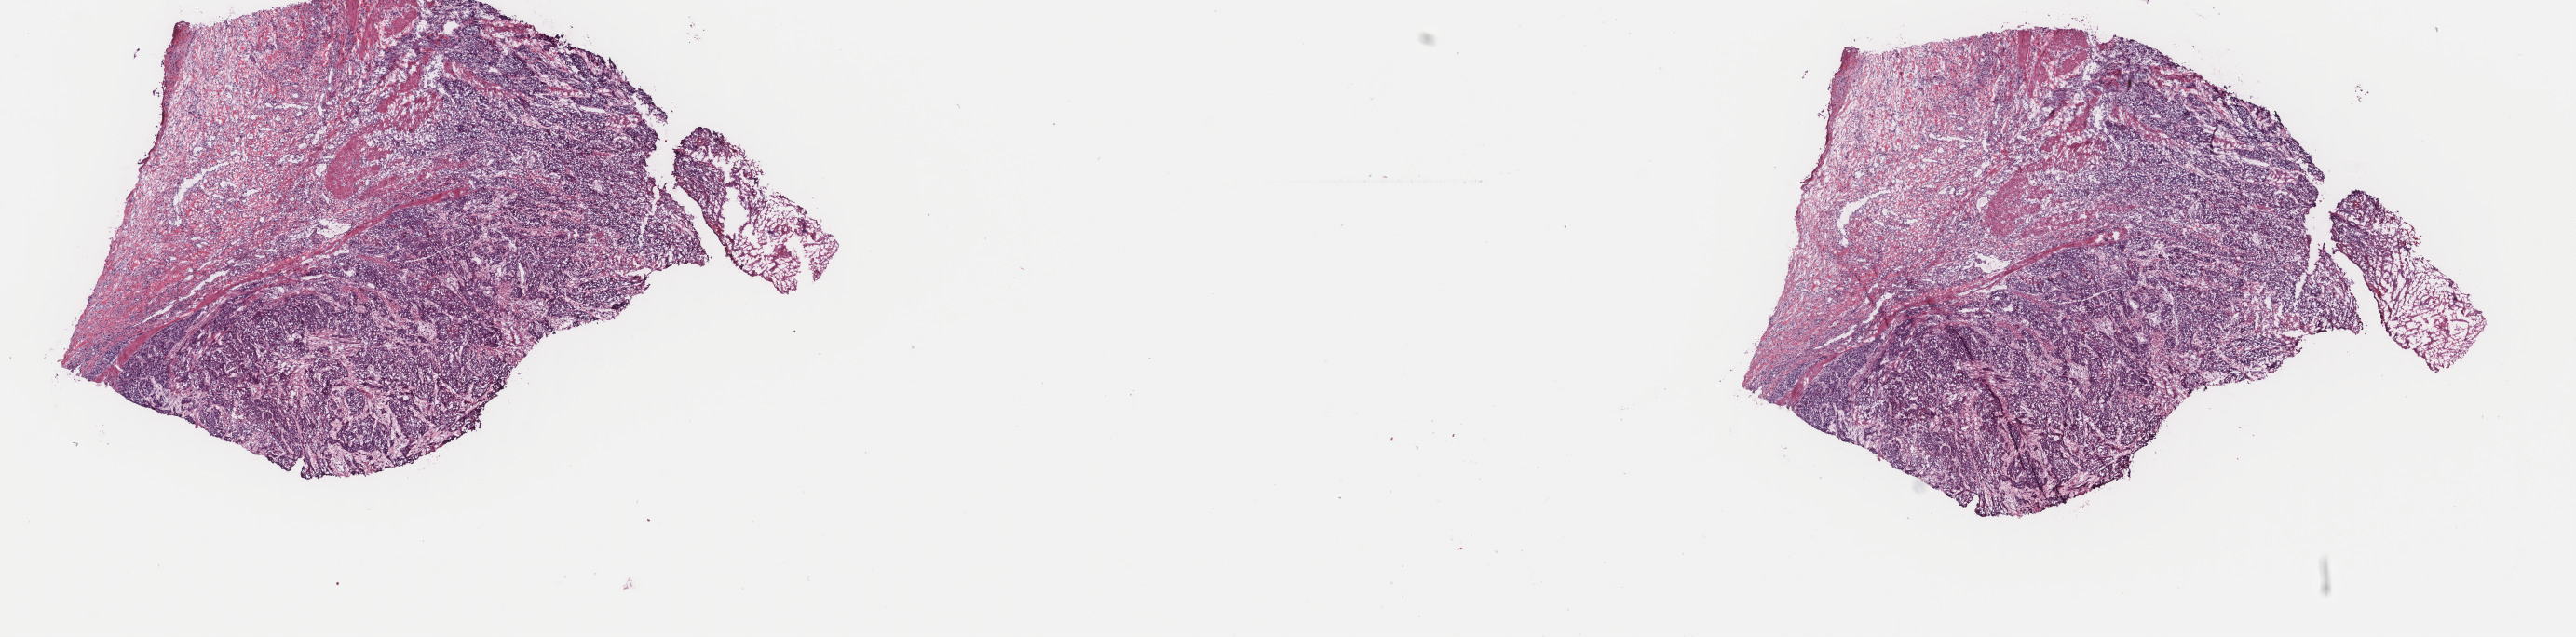
Whole-slide histology image, H&E-stained — shown as a low-resolution overview of the whole scanned area (about 22.0 x 5.4 mm, slide scanned at 40x); frozen section; primary tumour sample from the esophagus. Patient: male, age at initial diagnosis 54 years. Histologic grade: G1 (well differentiated). Composition of this section per pathologist review: tumour cells 100%, tumour nuclei 75%, normal cells 0%, stromal cells 0%, necrosis 0%. Inflammatory infiltration, as recorded: lymphocyte infiltration 3%, monocyte infiltration 0%, neutrophil infiltration 0%.
• AJCC pathologic stage: IIB (7th edition)
• pathologic diagnosis: Squamous cell carcinoma, keratinizing, NOS